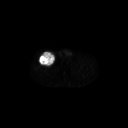
FDG PET of an extremity soft-tissue mass (from a PET/CT study), one axial slice. Slice 289 of 311 in the series (ordered by position). 128 × 128 image matrix, field of view 700 × 700 mm. Male patient, age 56 years. Case-level facts recorded for this patient, not image findings: histological type: pleiomorphic leiomyosarcoma; grade: intermediate; site of the primary tumour: right thigh.
Outlined on this slice (expert contour drawn on MRI and transferred to this co-registered scan by the dataset authors):
- gross tumour volume including surrounding oedema: bounding box (x1, y1, x2, y2) in pixels: (38, 52, 55, 66)
- gross tumour volume (mass): (39, 52, 55, 66)